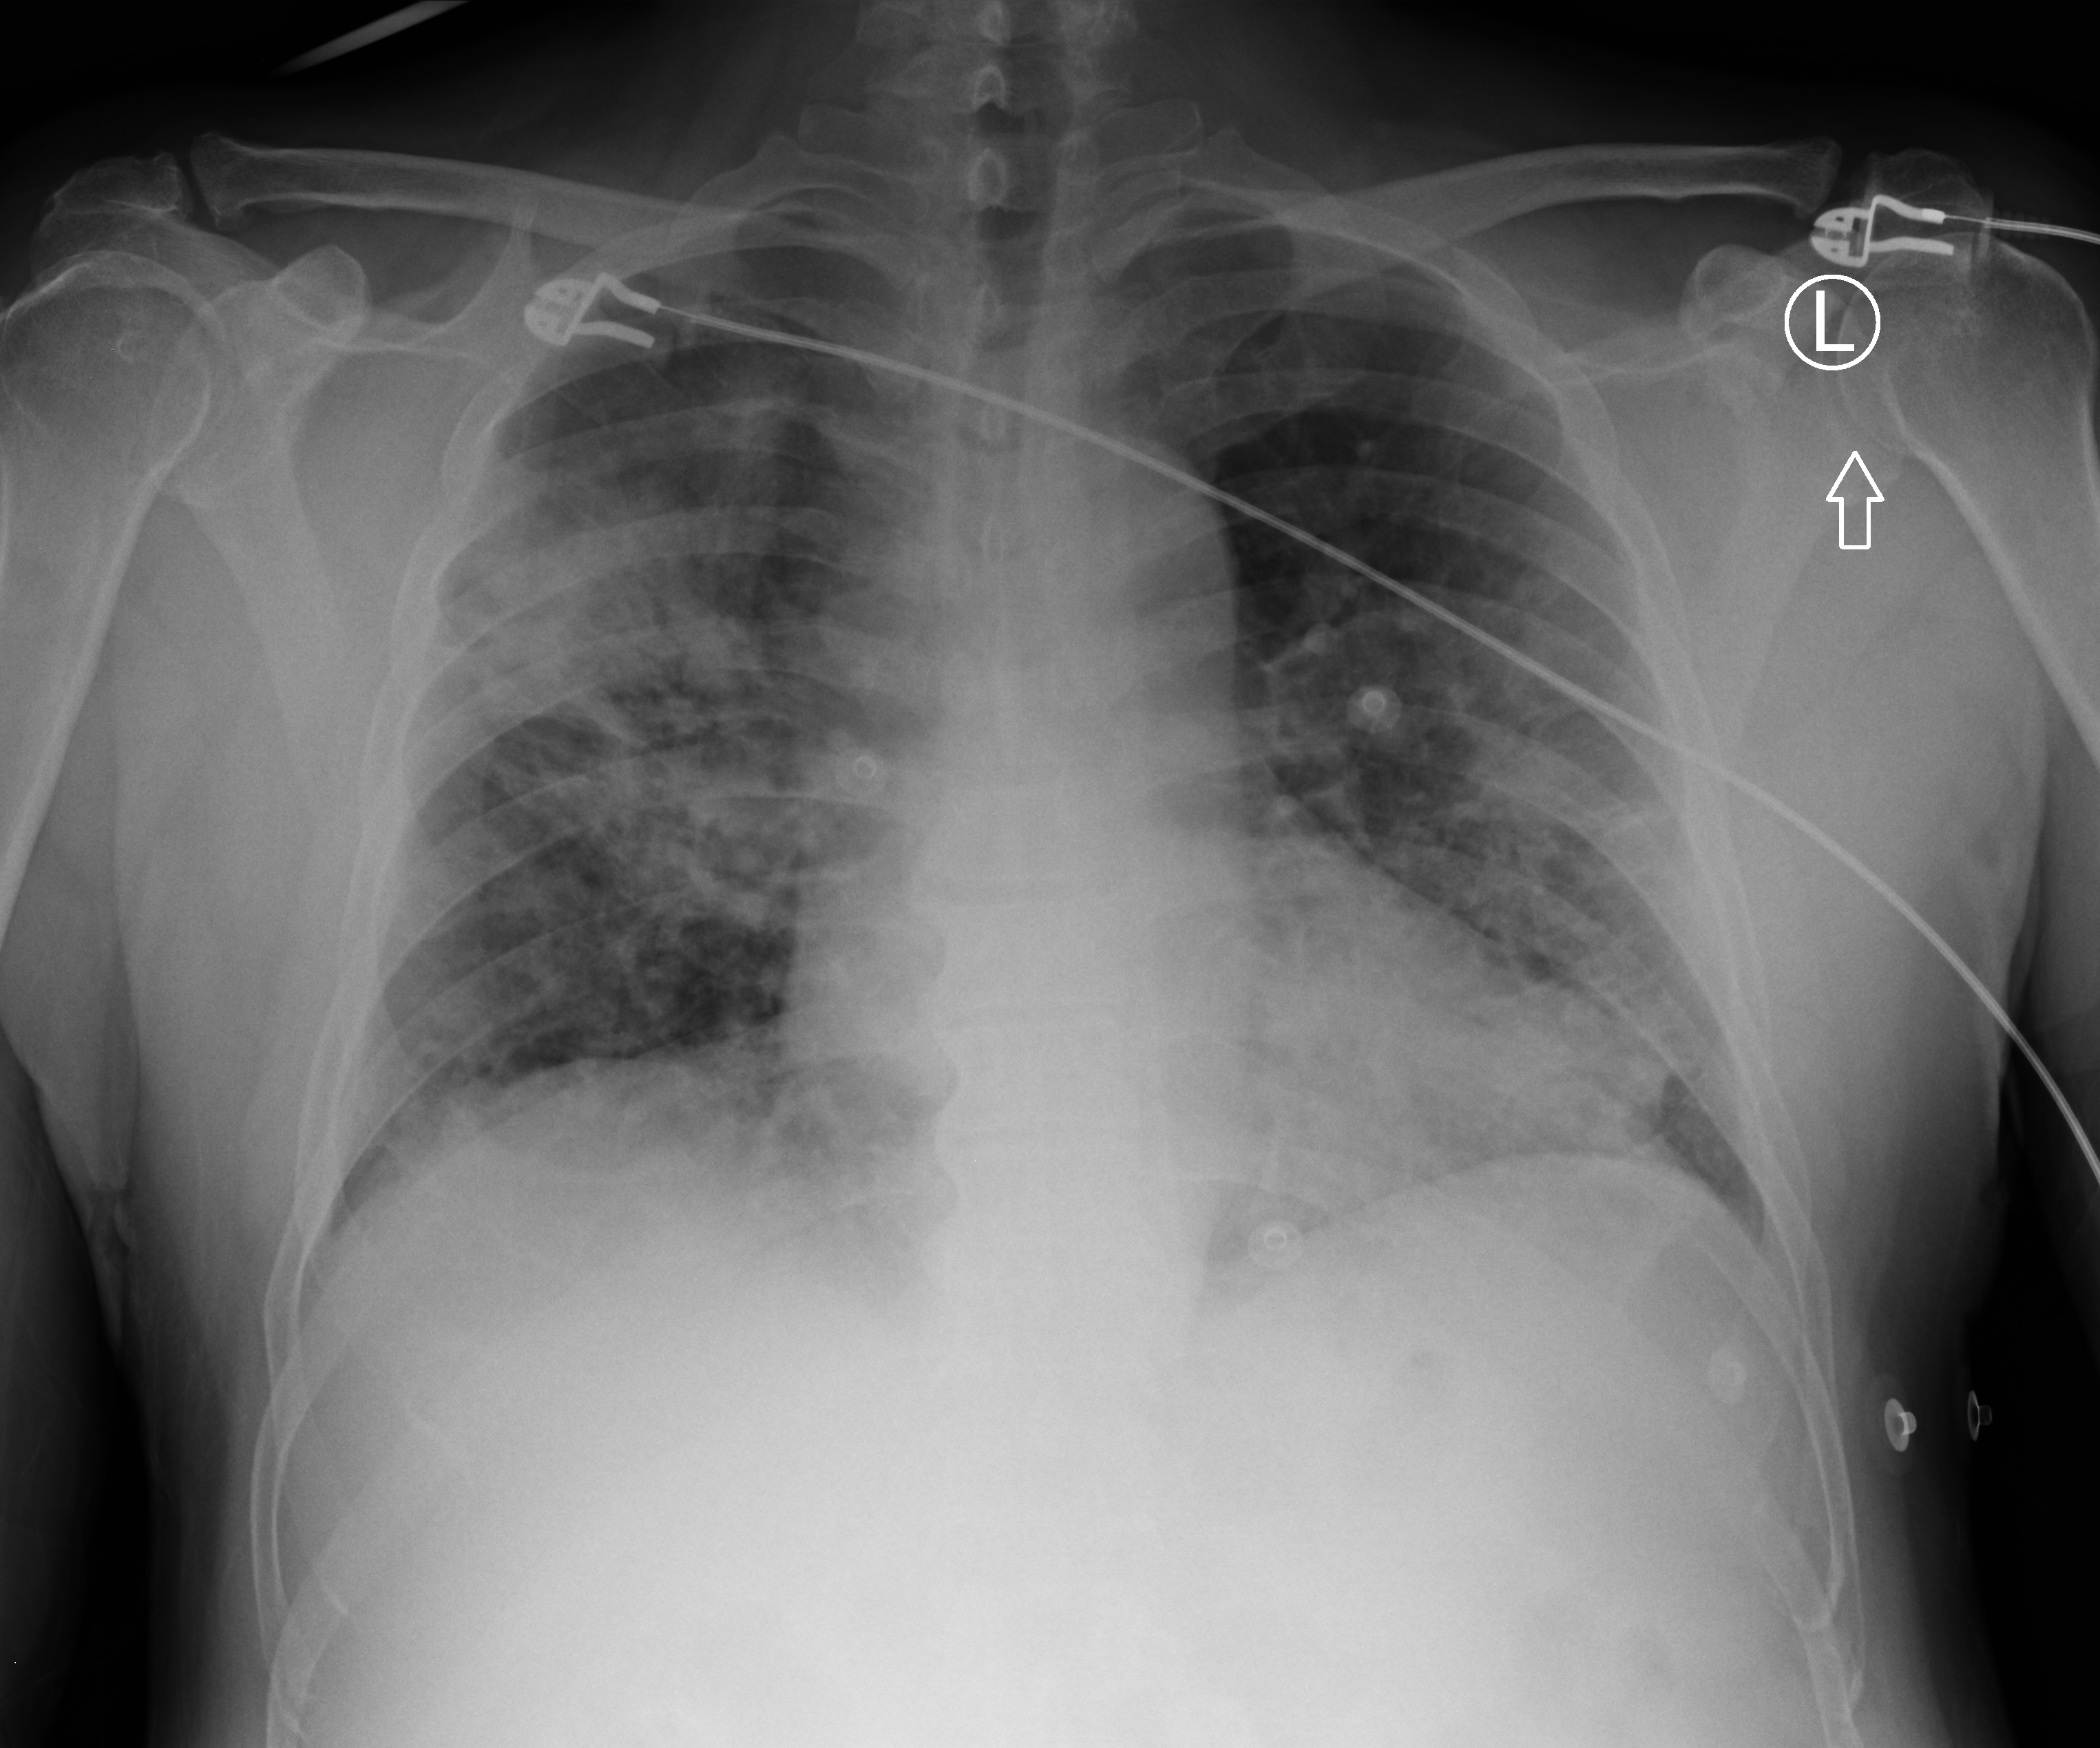
Chest X-ray (portable). Male patient hospitalised with COVID-19, age 18–59 years.
From the hospital-stay record, not from the radiograph (when in the stay this image was taken is not recorded): admitted to intensive care during this hospital stay: no; mechanically ventilated during this hospital stay: no.